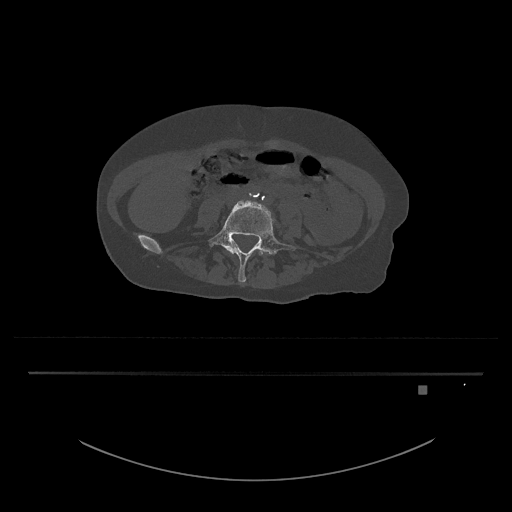
CT including the spine, one axial slice. Slice 312 of 797 in the series (ordered by position). Reconstruction kernel Br40s/3. Bone window (W 1800 / L 400 HU). 0.5 mm slice thickness. 512 × 512 image matrix. Female patient, age 57 years. Case-level facts recorded for this patient, not image findings: primary cancer: cervical.
Structures marked on this image (semi-automatic segmentation, software-assisted and operator-edited):
- L4 vertebra: bounding box <230,249,263,256> (left, top, right, bottom; pixels)